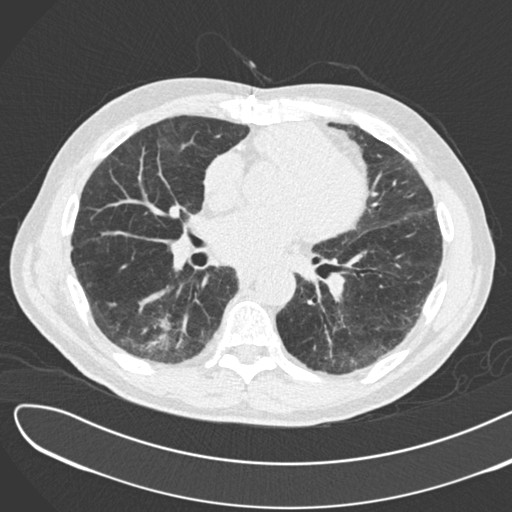
Low-dose screening chest CT, one axial slice; position 82 of 183 along the scan axis; lung window (W 1500 / L -600 HU); 512 × 512 image matrix.
Outlined on this slice (manually delineated by an expert):
- lesion 1 (tumor, lower lobe of right lung): bounding box (x1, y1, x2, y2) in pixels: (161, 318, 171, 331)